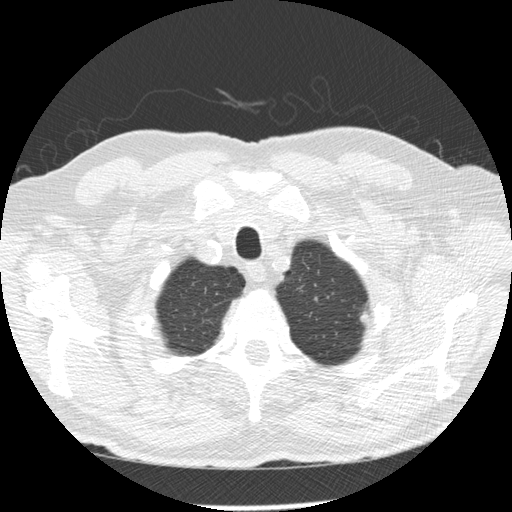
Chest CT (low-dose screening protocol), one axial image, third screening round (two years after baseline), lung window (W 1500 / L -600 HU), standard (soft-tissue) reconstruction kernel (STANDARD), slice 22 of 258 in the series. Male, age 73 years at enrolment. Former smoker at enrolment.
Expert-annotated lung lesion, bounding box <347,295,389,334> (left, top, right, bottom; pixels). The exam's reader record, not a measurement of the box and not confirmed to be the same lesion: non-calcified nodule or mass ≥4 mm, left upper lobe, 8 × 7 mm, poorly defined margins, mixed attenuation, pre-existing on the prior screen: no. Official screen result: positive, other. Participant outcome: lung cancer diagnosed 93 days after this screen — adenocarcinoma, NOS, left upper lobe, poorly differentiated (G3), stage IB (AJCC 6th edition), 10 mm at pathology.